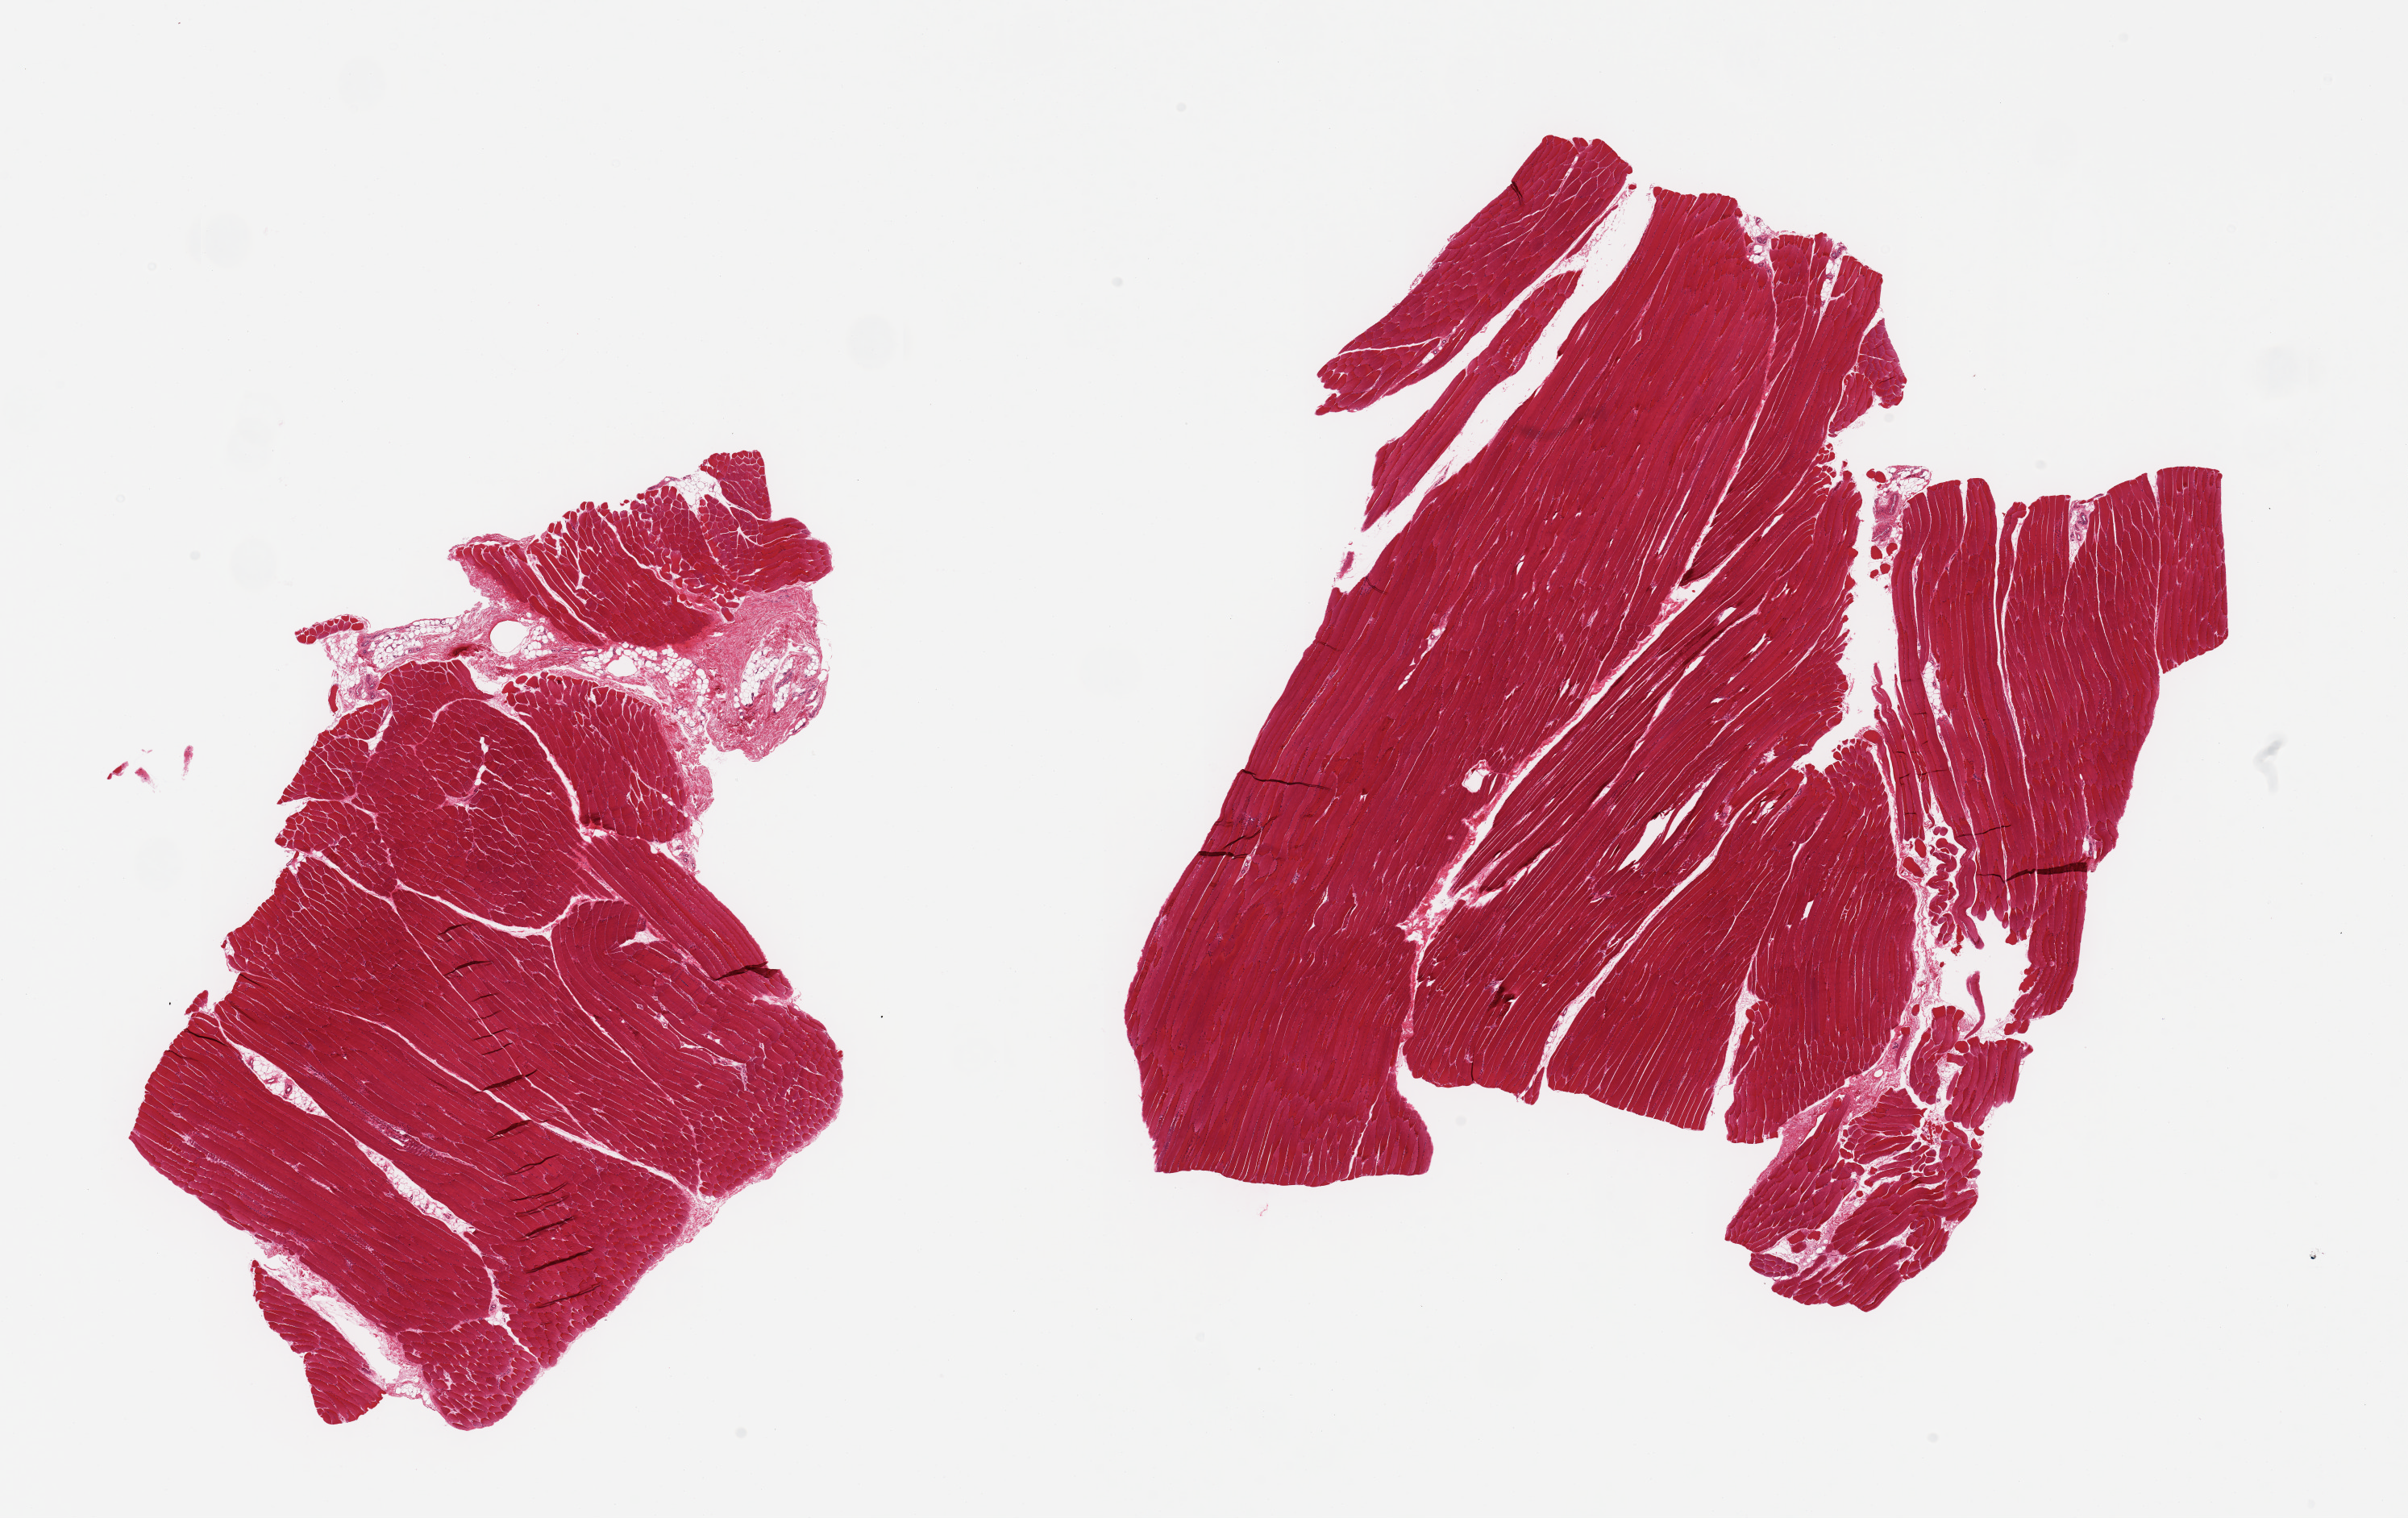
Whole-slide image, H&E stain, brightfield — whole scanned area (about 23.6 x 14.9 mm) shown as a low-resolution overview. PAXgene-fixed paraffin-embedded (PFPE) section. Section of skeletal muscle (target tissue). Donor tissue sample. Donor: male.
Reviewer comment on this tissue sample: 2 pieces.